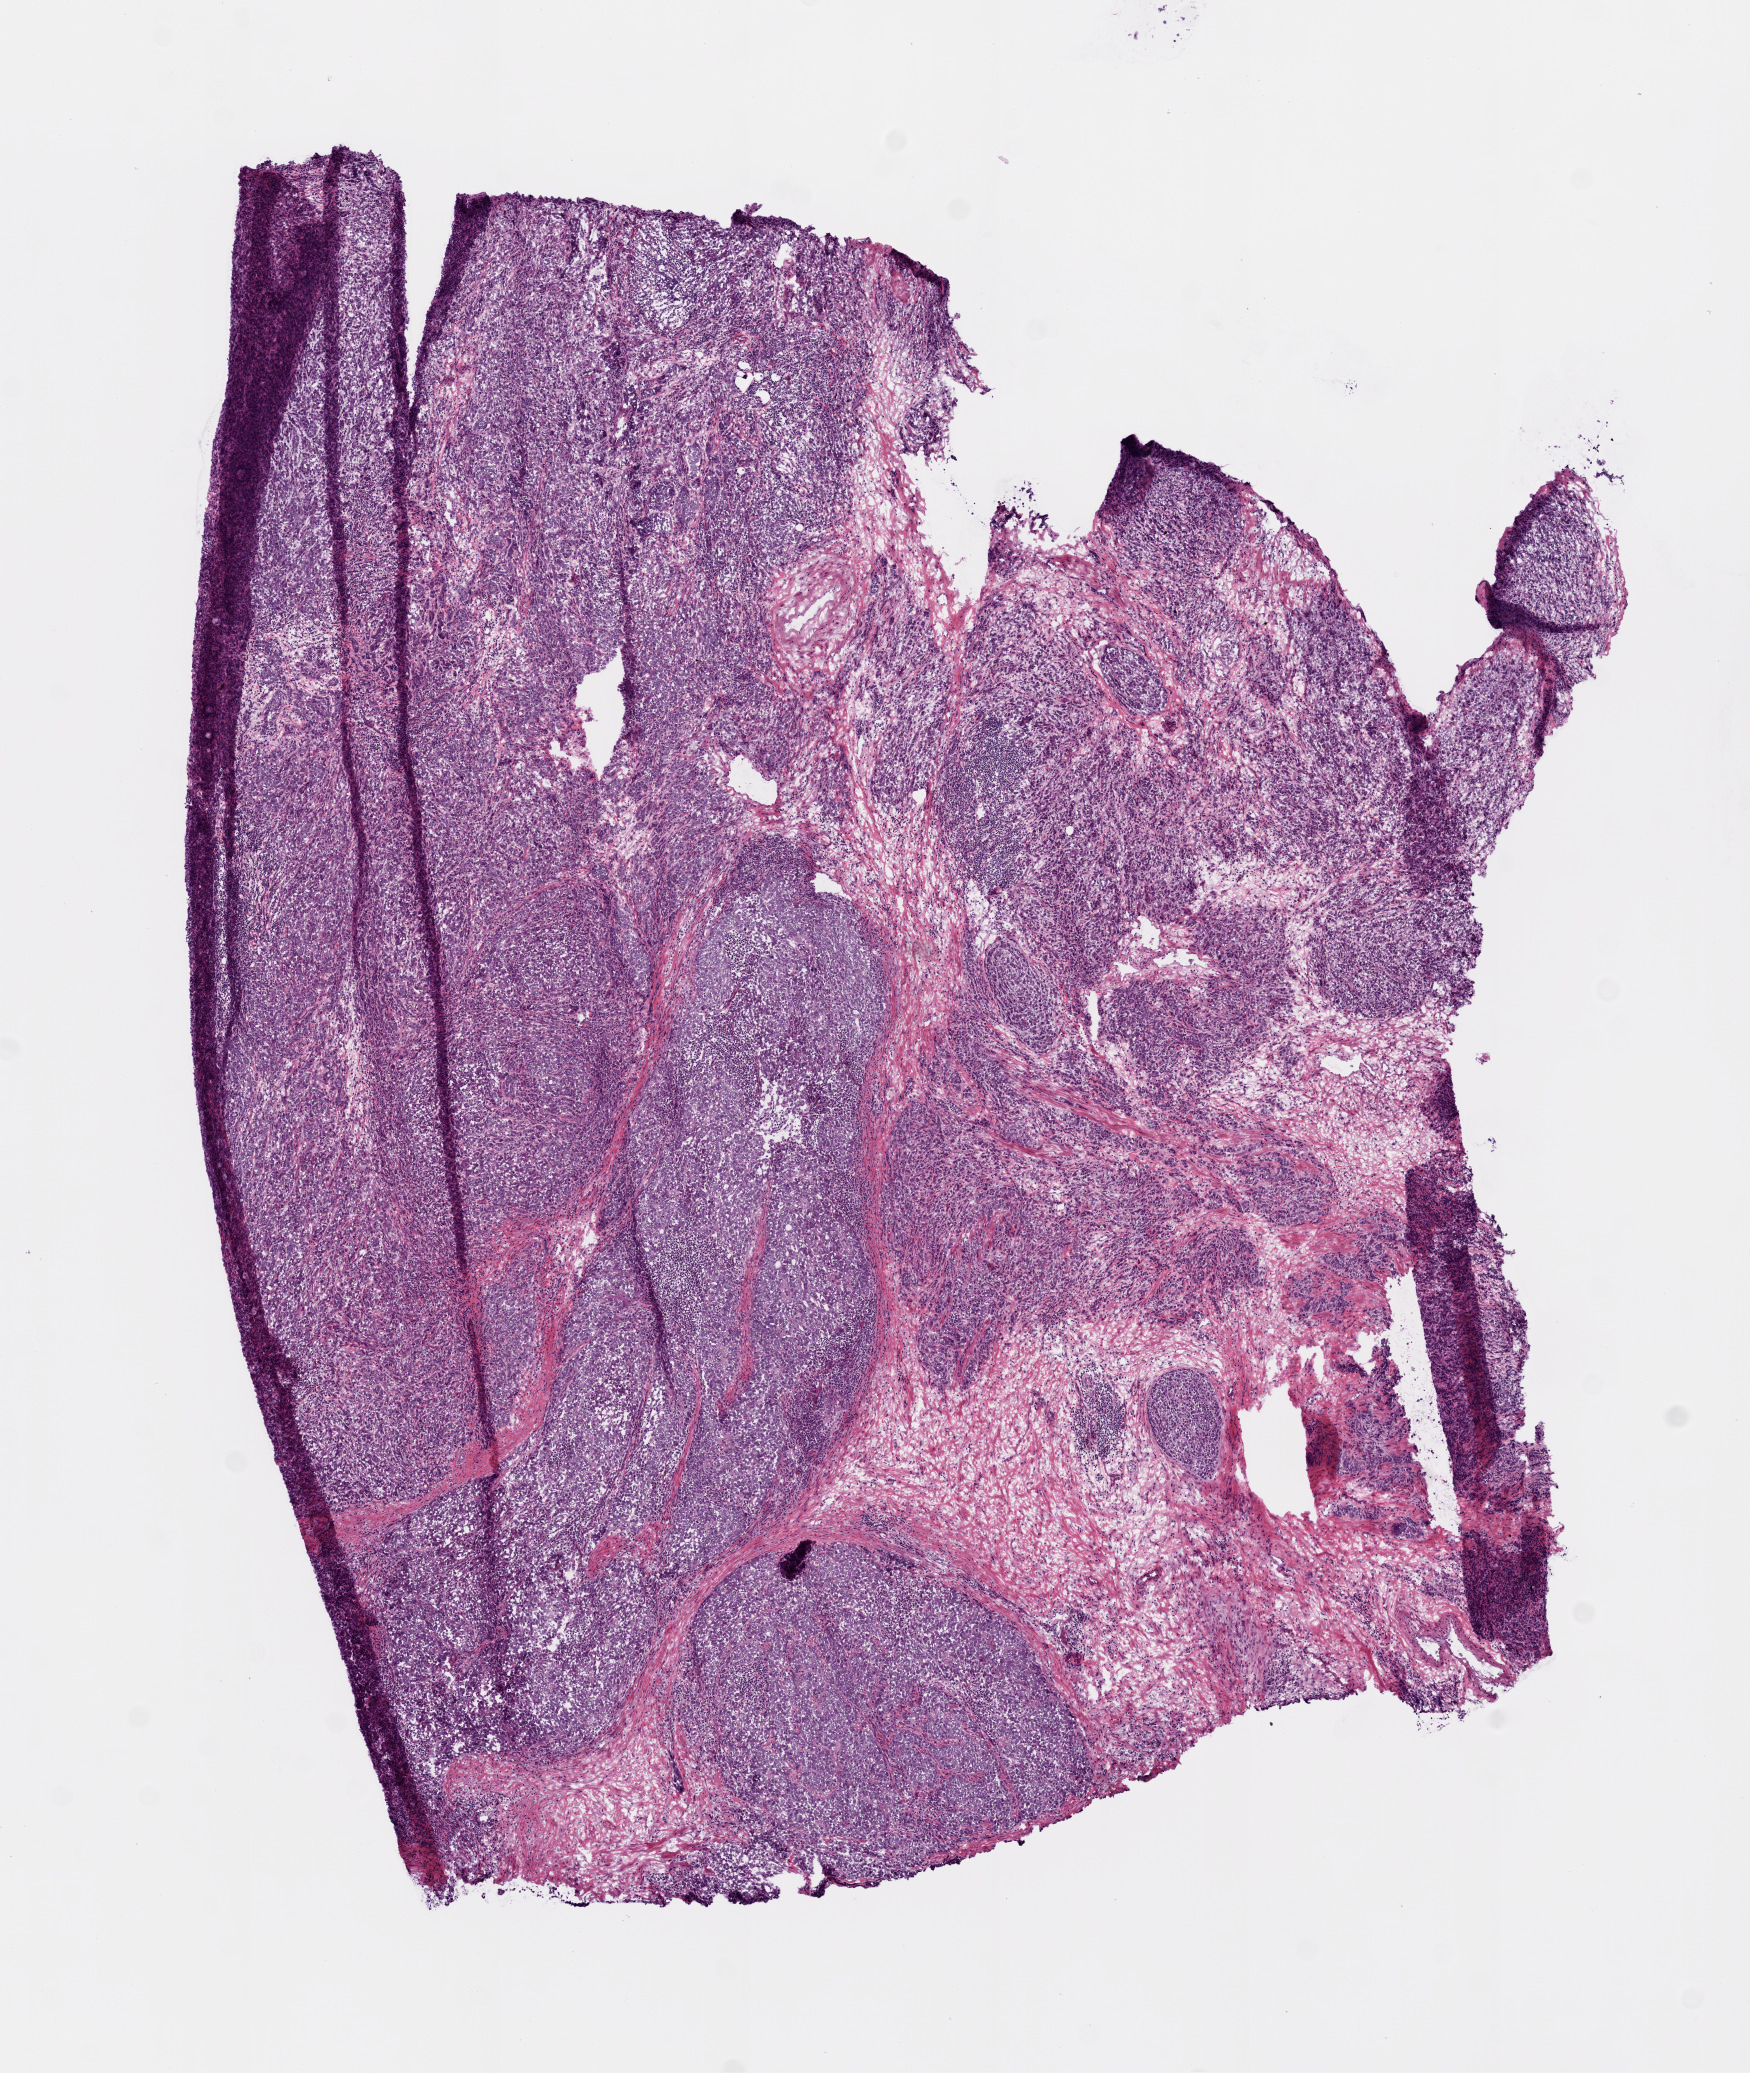
Digitized H&E tissue section (whole slide), a low-resolution overview of the entire scanned area, about 7.0 x 8.3 mm (acquisition: 20x scan), frozen section from the top of the tissue portion, sample: primary tumour, prostate. Patient: male, age at initial diagnosis 68 years. Gleason score: 10 (5+5). Pathologist review of this section (percent, as recorded): tumour cells 85%, tumour nuclei 90%, normal cells 0%, stromal cells 15%, necrosis 0%. Inflammatory infiltration, as recorded: lymphocyte infiltration 0%, monocyte infiltration 0%, neutrophil infiltration 0%.
• laterality: bilateral
• lymph nodes positive (case pathology): 1 of 3 examined
• pathologic diagnosis: Acinar cell carcinoma (prostate gland)